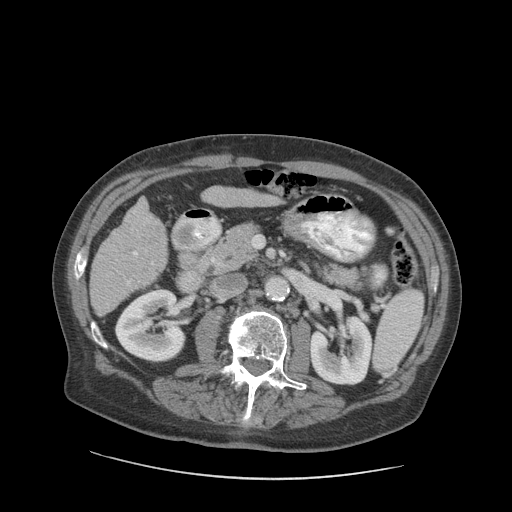
Contrast-enhanced abdominal CT (liver protocol), one axial slice. Slice 36 of 89 in the series (ordered by position). 140 kVp. Soft-tissue window (W 400 / L 40 HU). 2.5 mm slice thickness. 512 × 512 image matrix. Case-level facts recorded for this patient, not image findings: diagnosis: hepatocellular carcinoma (patient treated with transarterial chemoembolisation; whether this scan precedes or follows treatment is not stated here); TNM stage (as recorded): Stage-I; Child-Pugh class: A; tumour differentiation: moderately differentiated; tumour nodularity: uninodular.
Outlined on this slice (semi-automatic segmentation, software-assisted and operator-edited):
- liver parenchyma outside the tumour (the mass and vessels are separate outlines, so this box may not span the whole liver): bounding box (x1, y1, x2, y2) in pixels: (90, 198, 166, 316)
- mass: (123, 210, 164, 252)
- liver vessels: (127, 252, 154, 286)